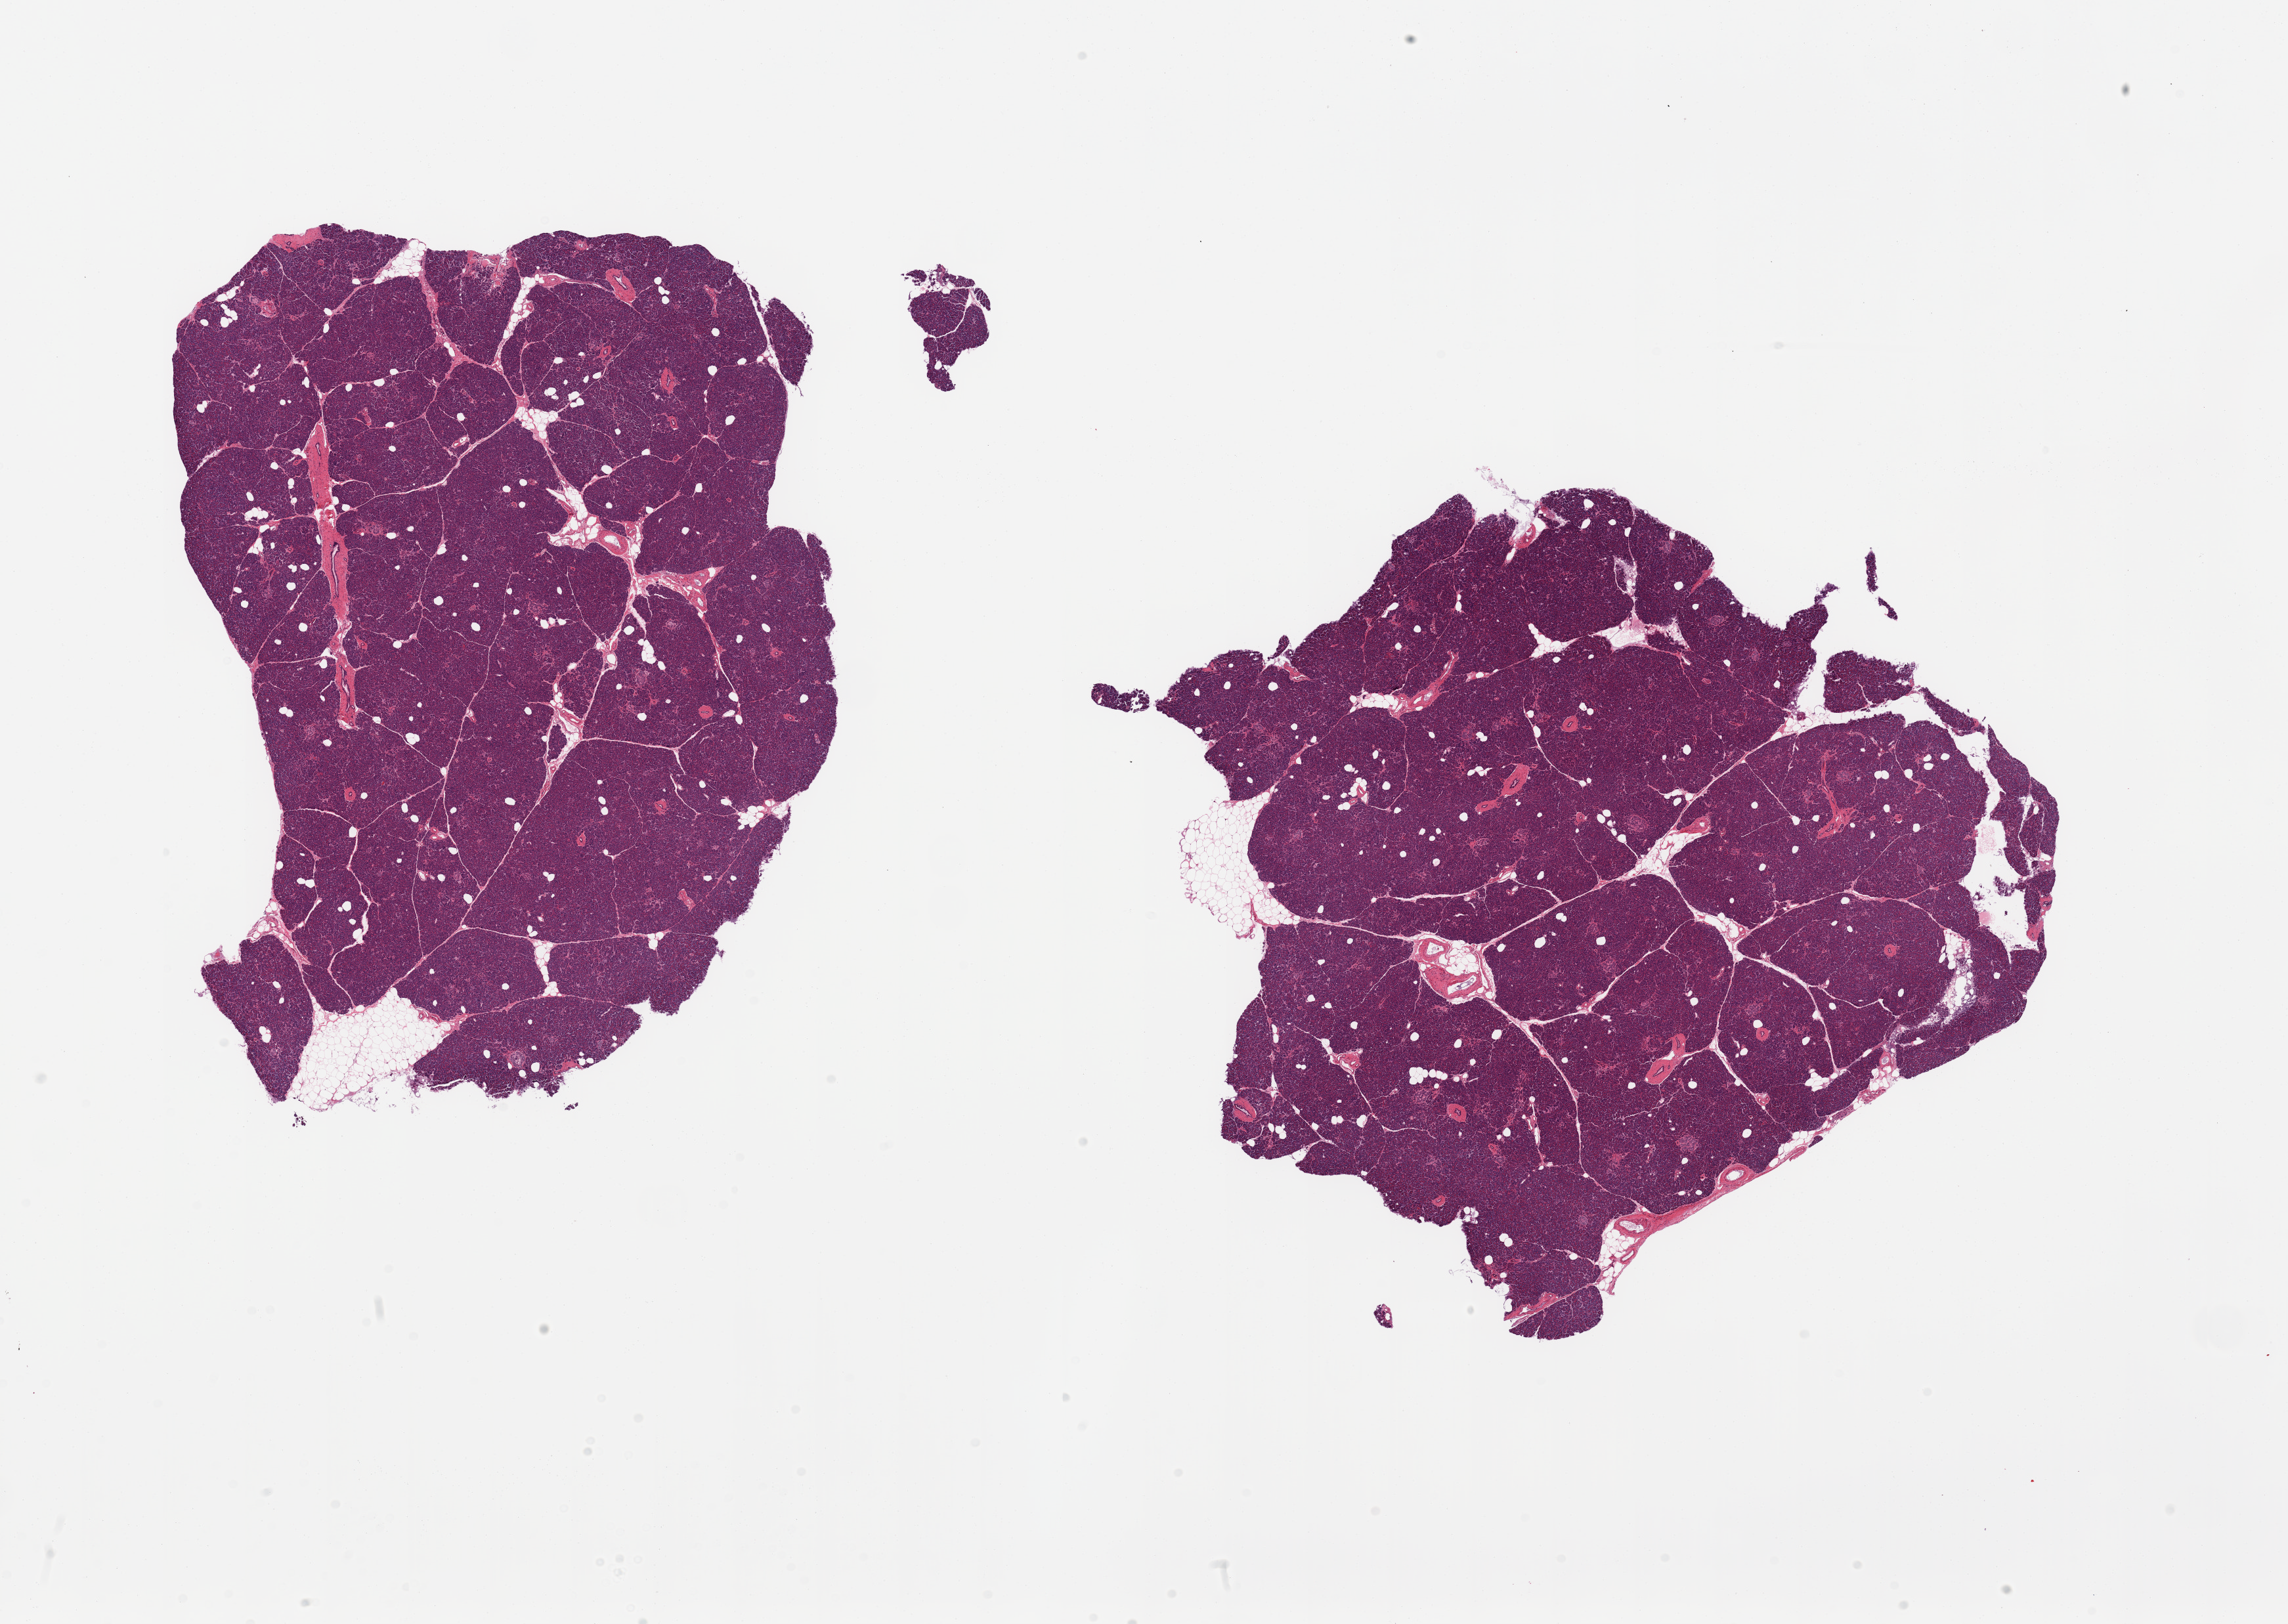
Haematoxylin and eosin whole-slide image — whole scanned area (about 27.6 x 19.6 mm, slide scanned at 20x) shown as a low-resolution overview; PAXgene-fixed, paraffin-embedded tissue; sampled site (target tissue): pancreas; donor tissue sample. Donor: female.
* pathologist's review note for this sample: 2 pieces, minimal attached and internal fat